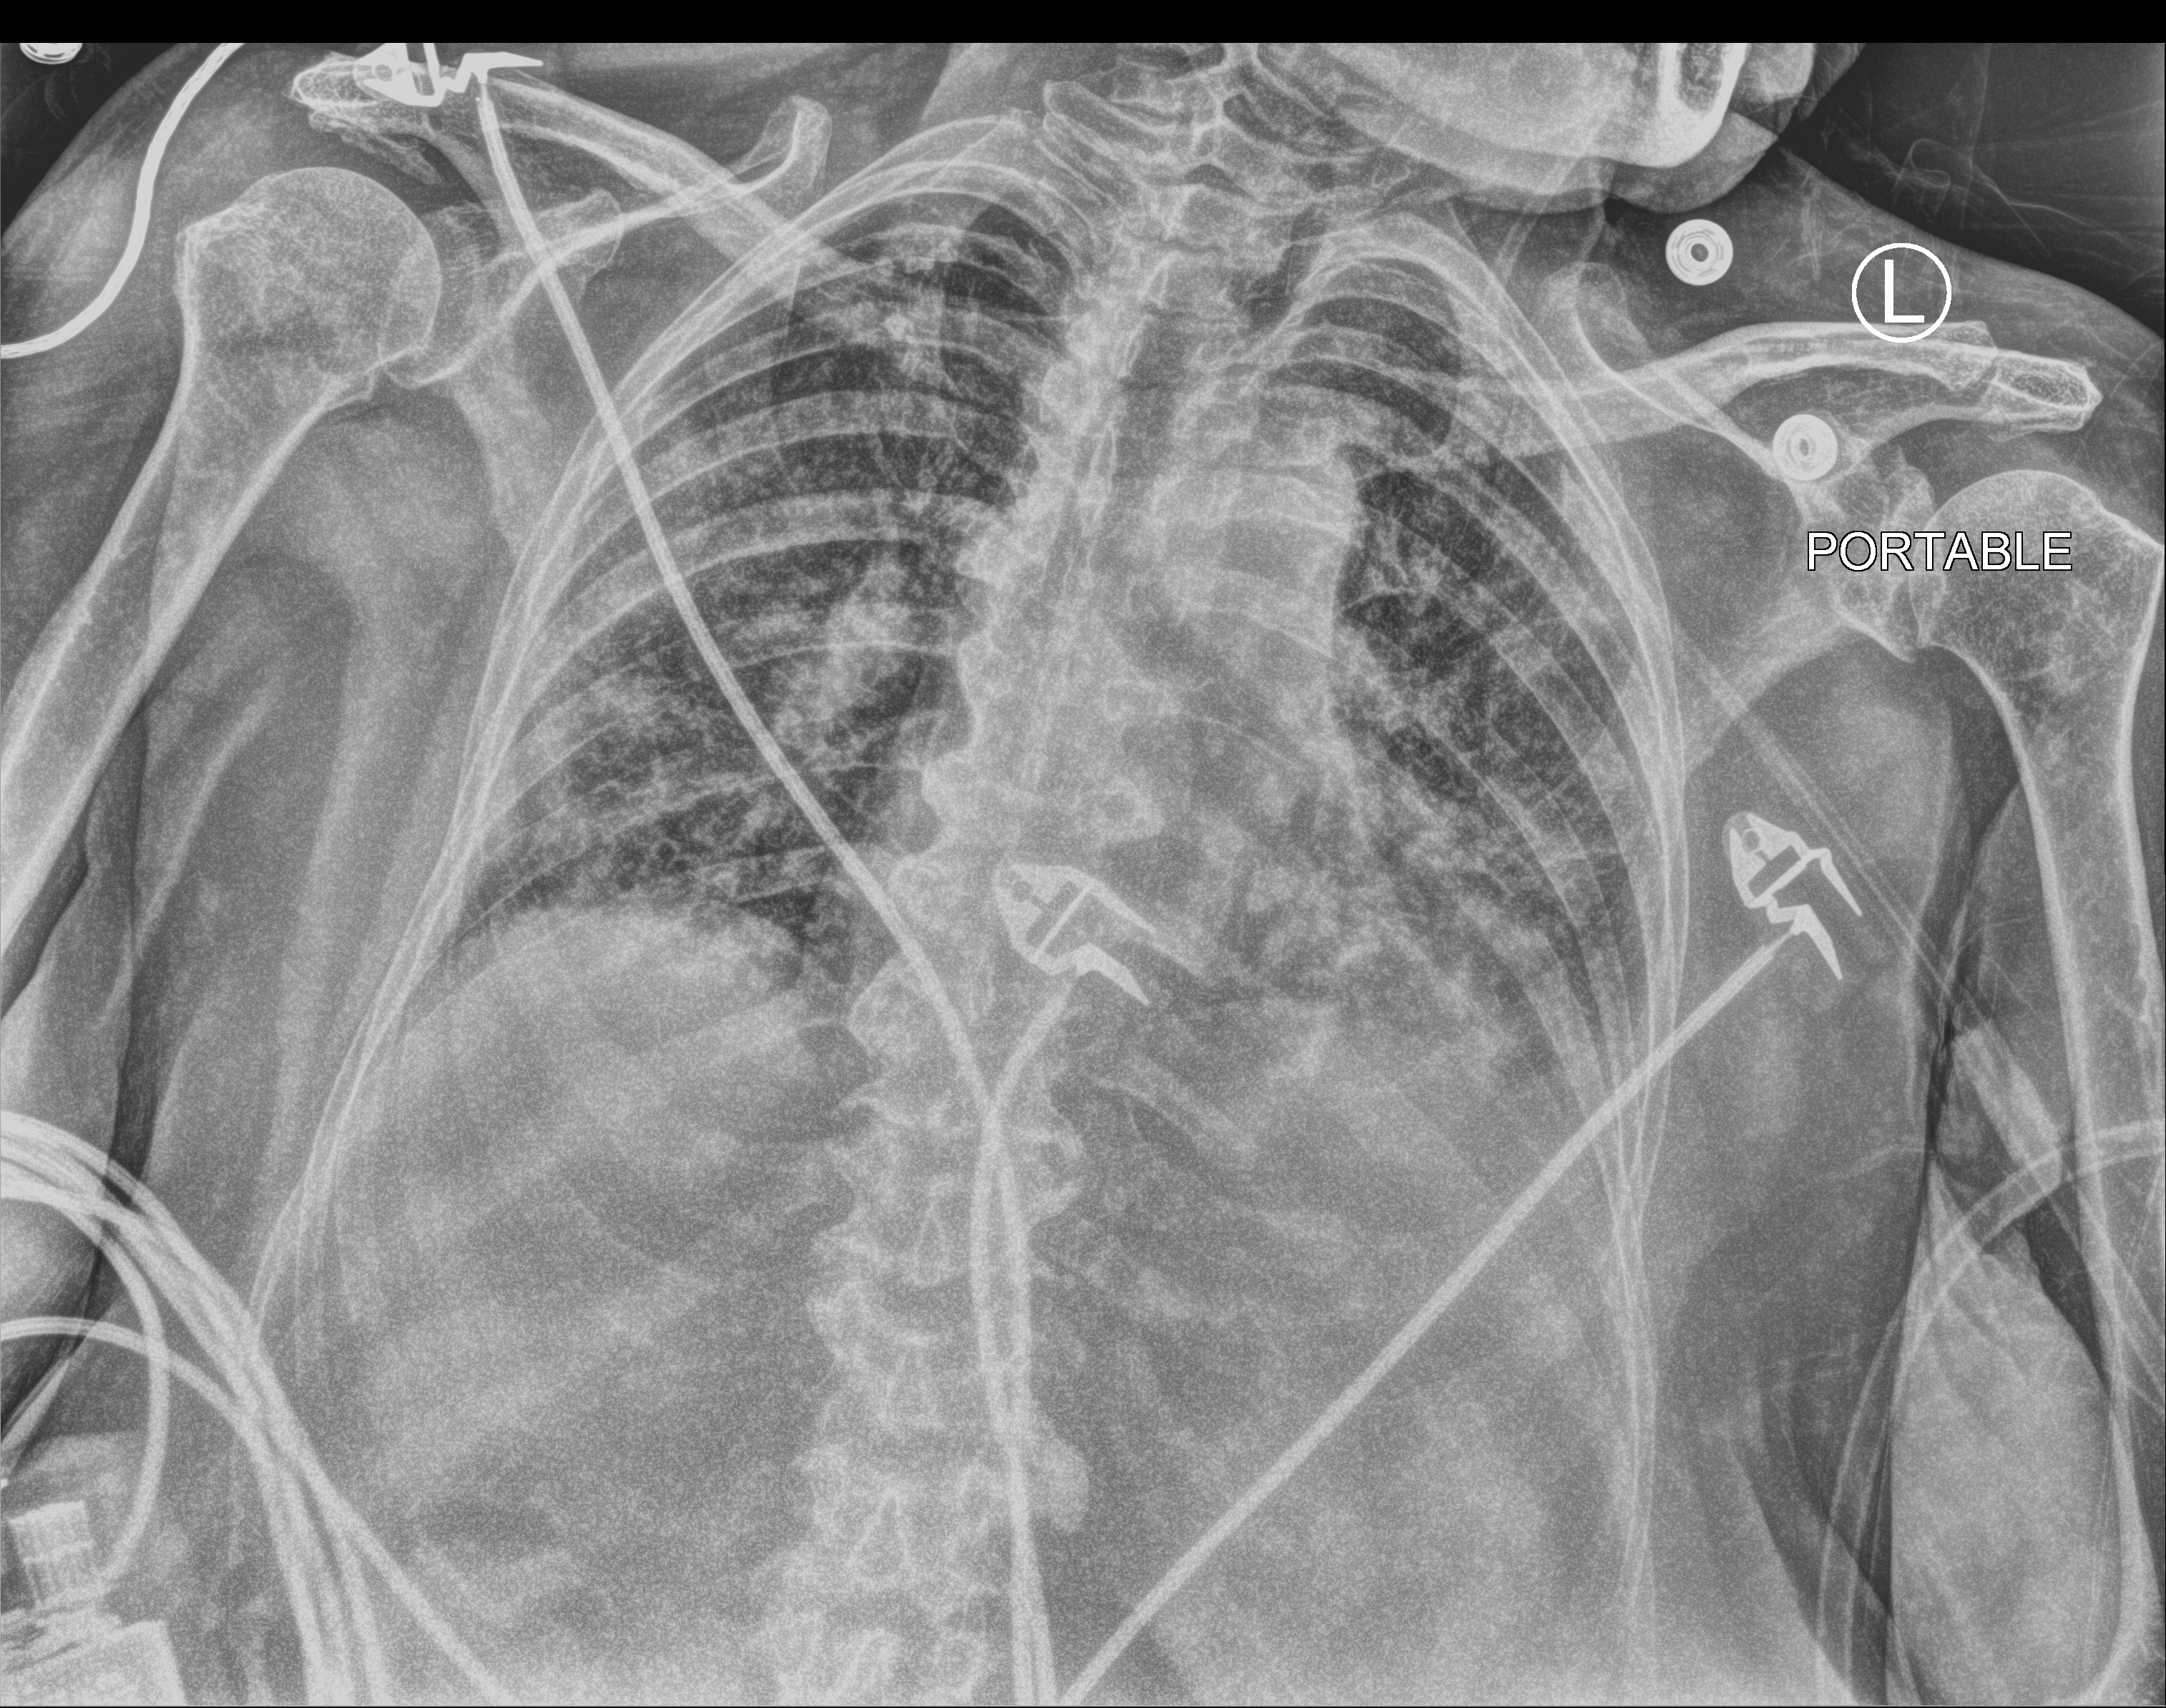
Bedside chest radiograph (computed radiography), anteroposterior (AP) projection. Female patient hospitalised with COVID-19, age 75–90 years.
From the hospital-stay record, not from the radiograph (when in the stay this image was taken is not recorded):
- admitted to intensive care during this hospital stay: yes